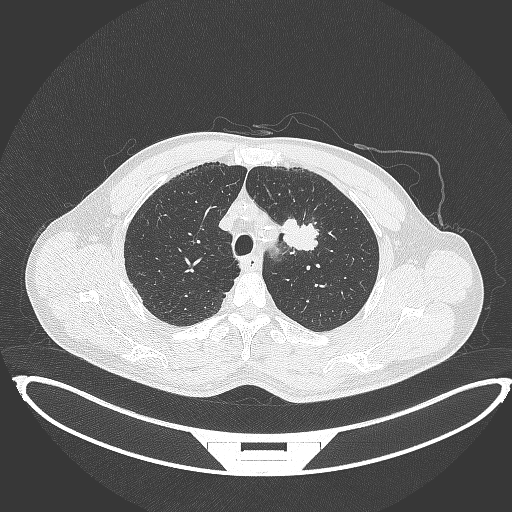
Chest CT, one axial slice. Position 342 of 395 along the scan axis. Reconstruction kernel B70f. Lung window (W 1500 / L -600 HU). 512 × 512 image matrix, field of view 457 × 457 mm. Patient: male, 60 years. Case-level facts recorded for this patient, not image findings: clinical TNM (as recorded): T2a N0 M0.
Outlined on this slice (rectangle marked by the reading radiologist):
- lung tumour (recorded histology: squamous cell carcinoma): bounding box <279,210,321,254> (left, top, right, bottom; pixels)